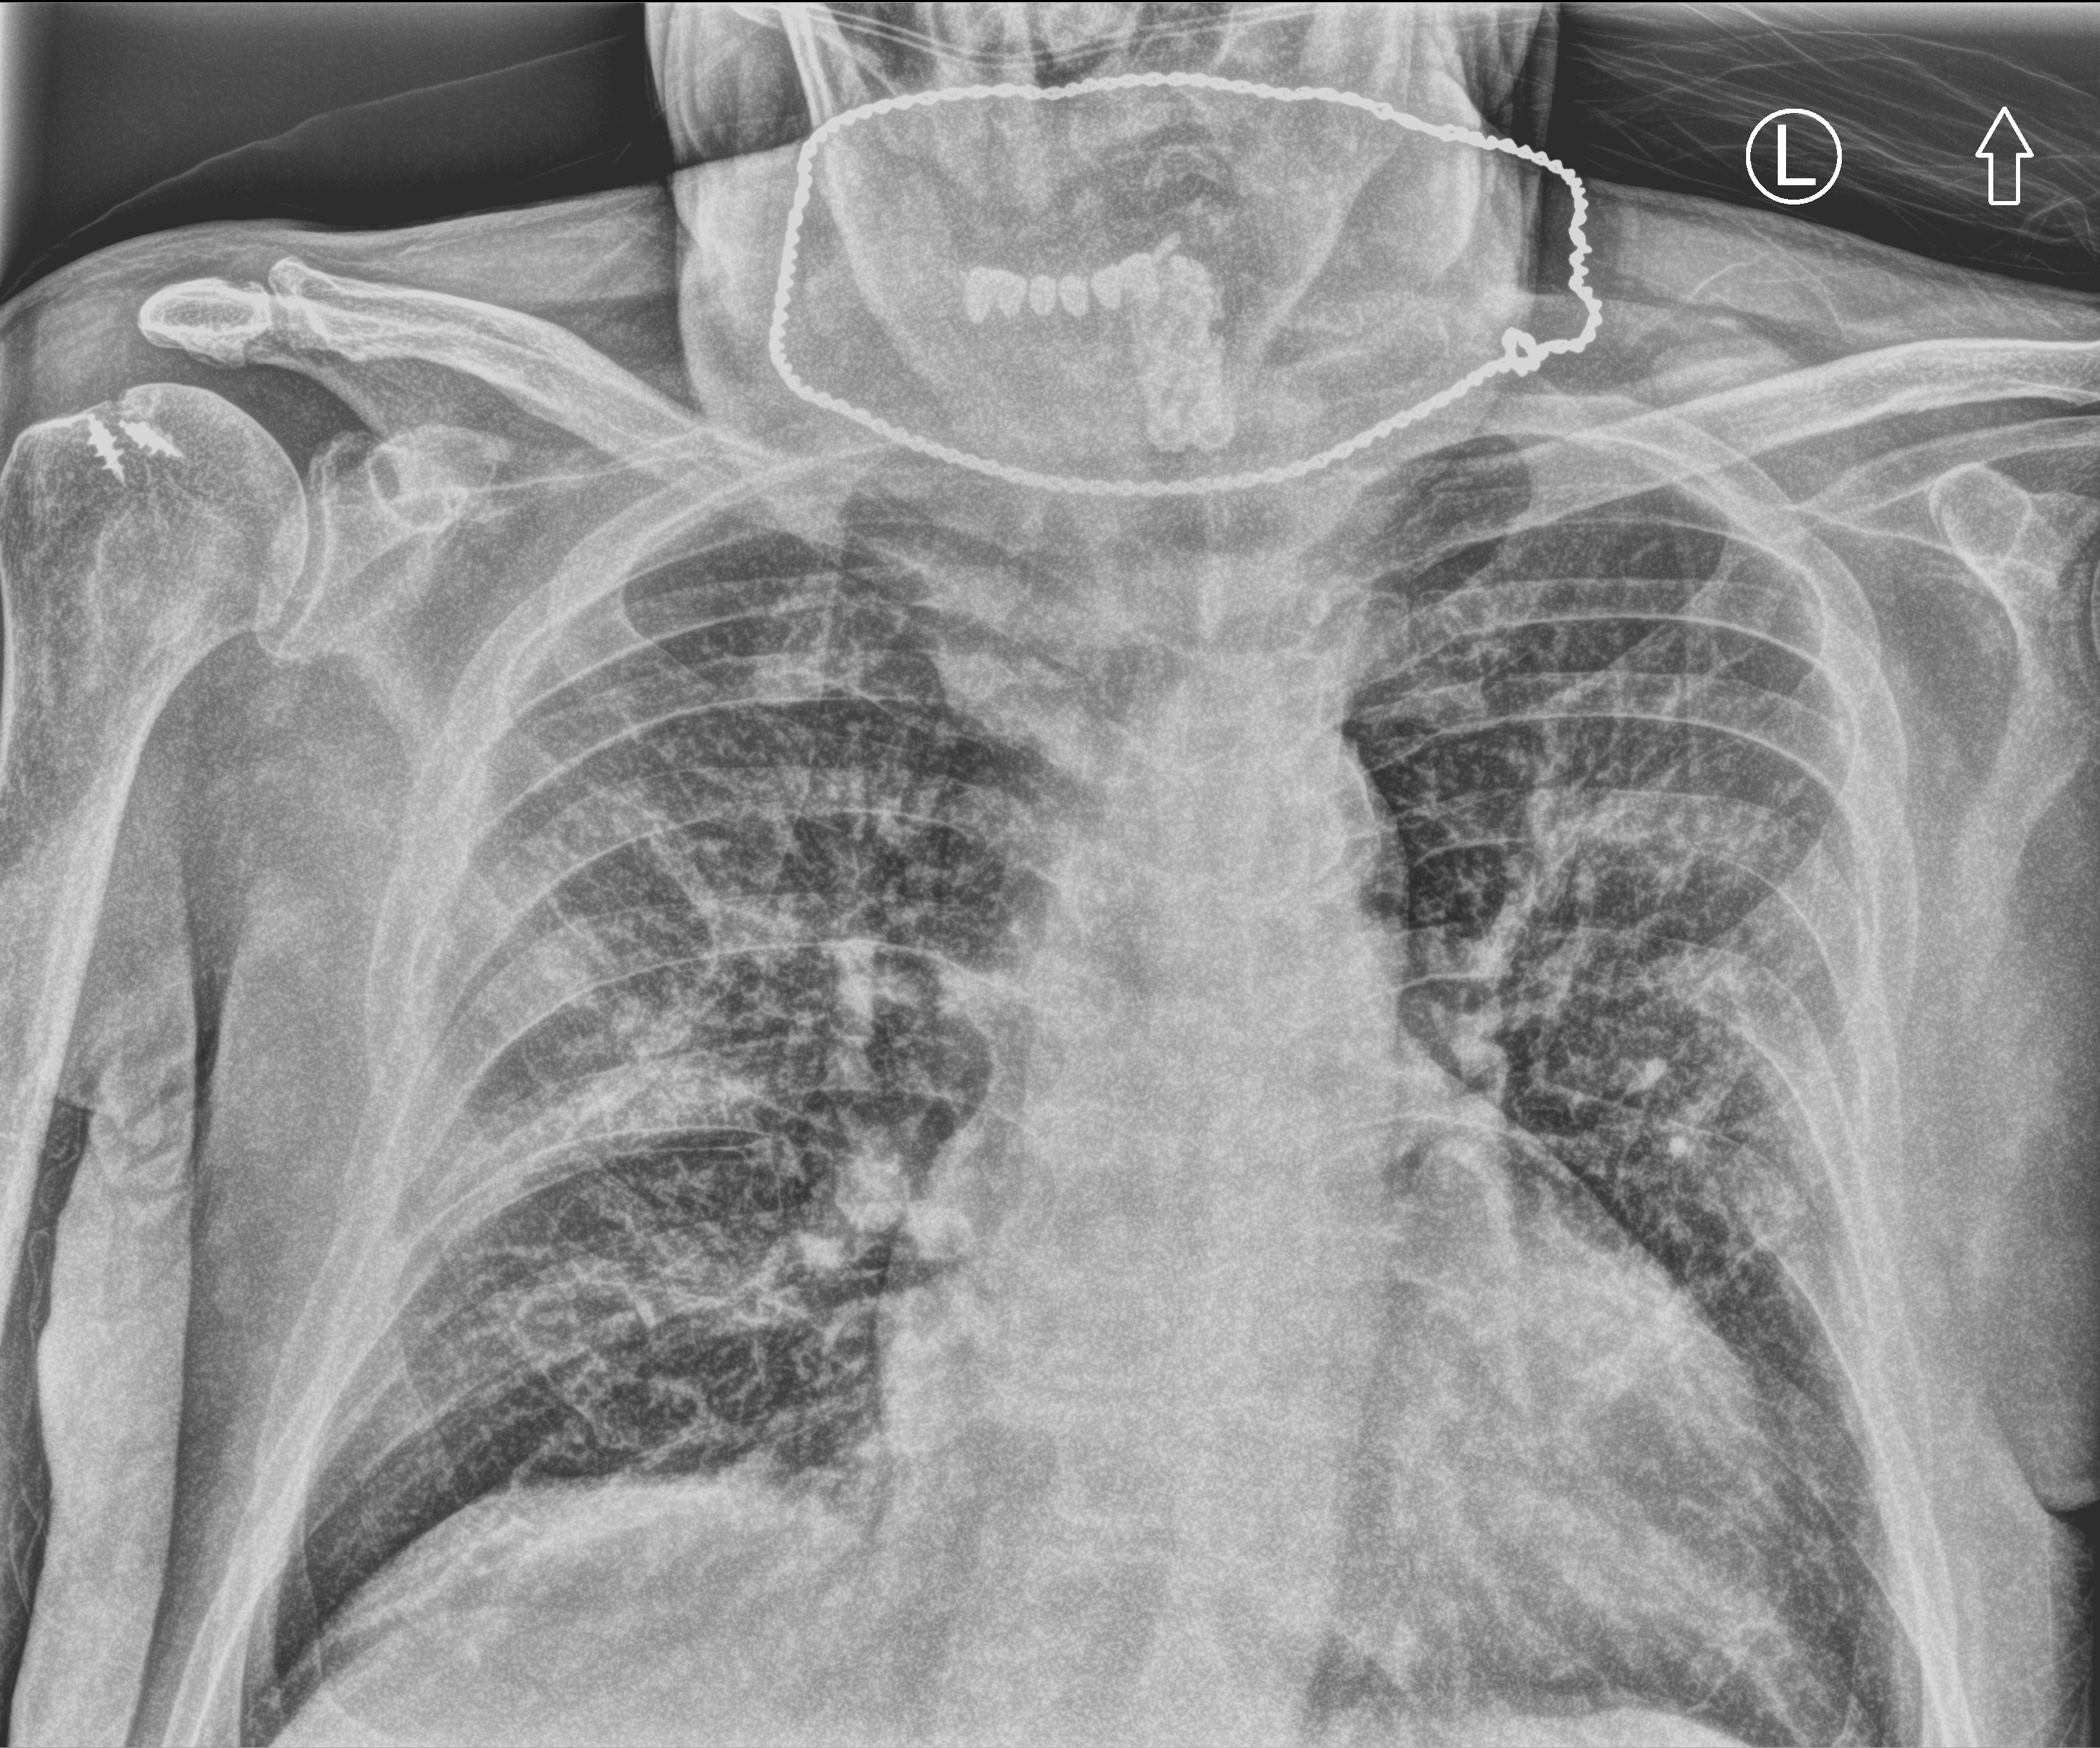
Chest X-ray (portable), anteroposterior (AP) projection. Male patient hospitalised with COVID-19, age 75–90 years.
Hospital-stay facts (about this admission, not read from this image; timing relative to this image not recorded):
- chronic kidney disease (admission record): no
- smoking status (admission record): former